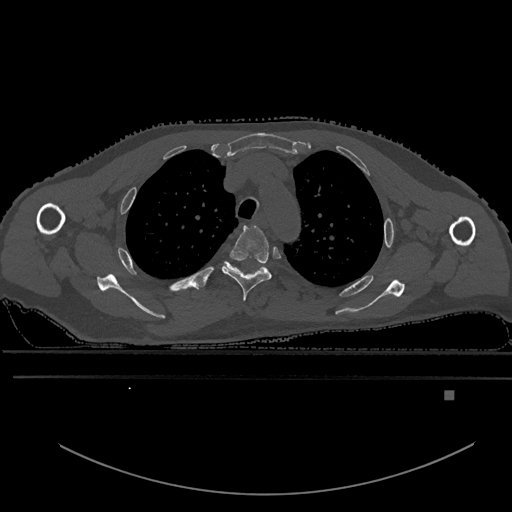
CT including the spine, one axial slice. Slice 444 of 969 in the series (ordered by position). Bone window (W 1800 / L 400 HU). 0.5 mm slice thickness. 512 × 512 image matrix, field of view 456 × 456 mm. Male patient, age 82 years. Case-level facts recorded for this patient, not image findings: primary cancer: prostate.
Annotated regions visible in this slice (semi-automatic segmentation, software-assisted and operator-edited):
- T3 vertebra: box from (x=221, y=225) to (x=272, y=301) px
- T4 vertebra: (x=226, y=262)–(x=268, y=272)